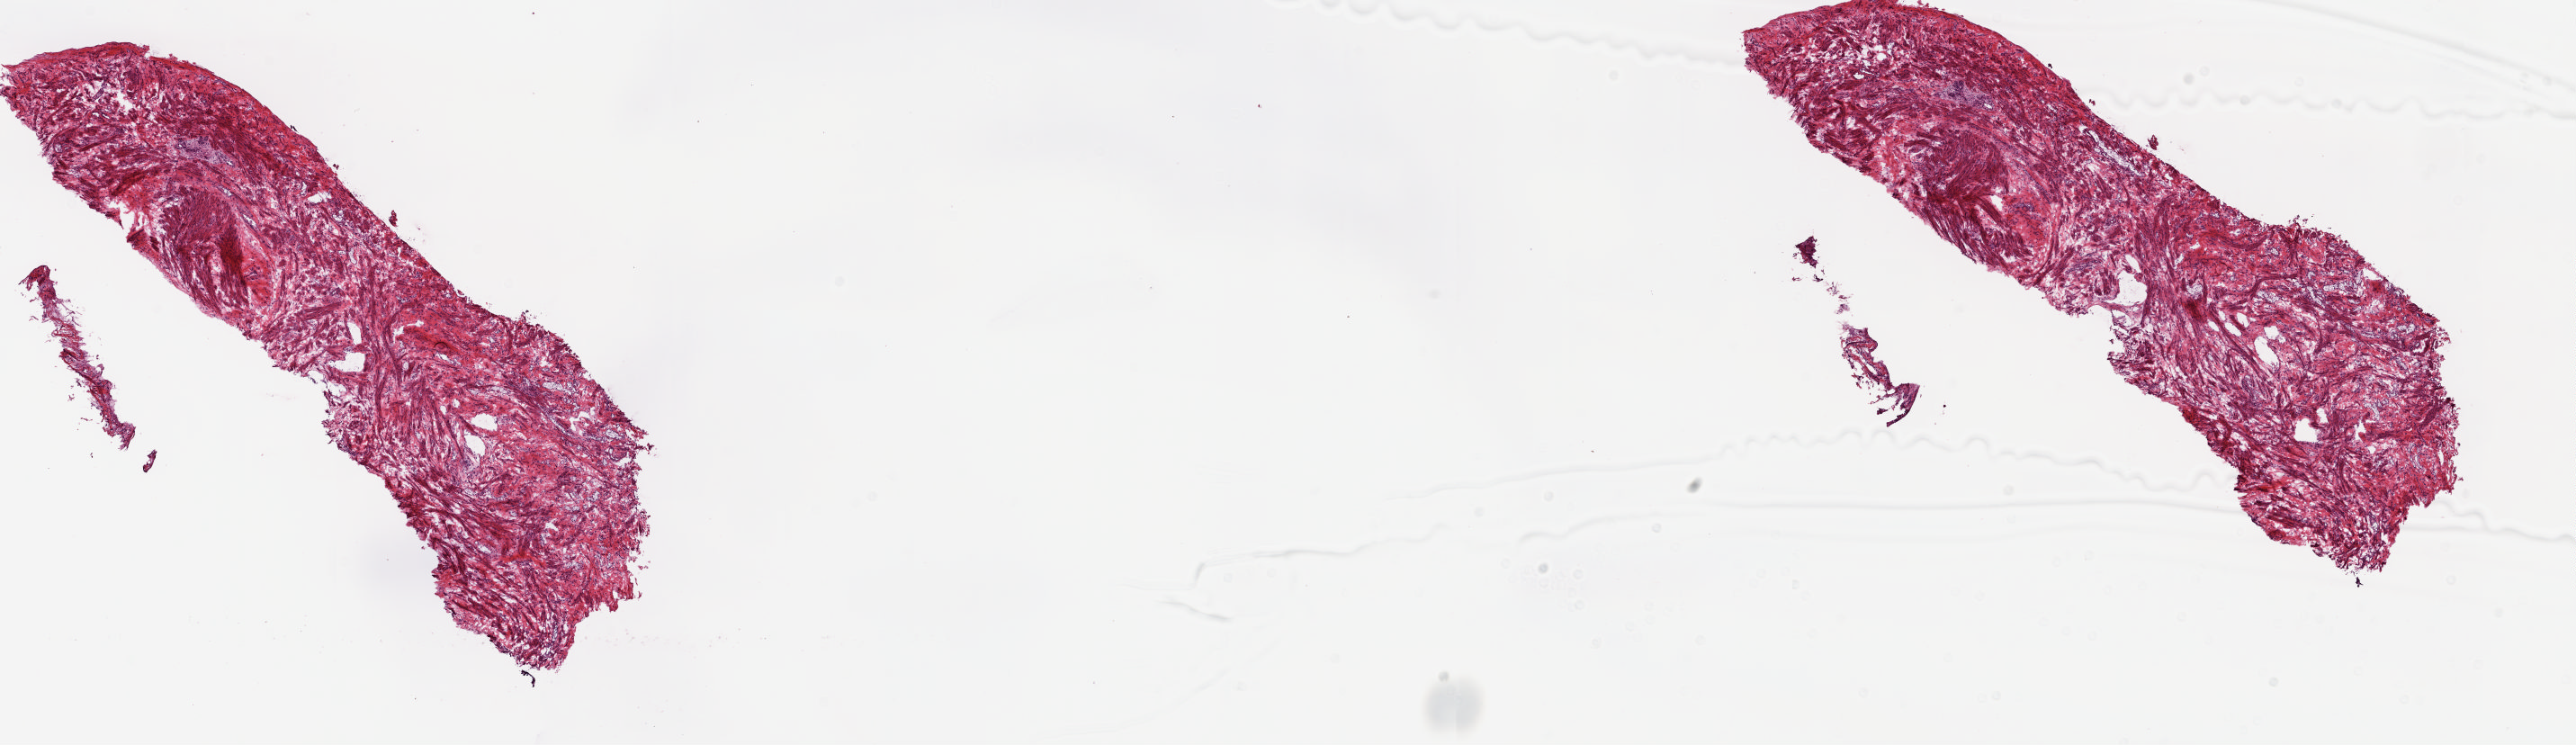
Whole-slide histology image, Hematoxylin and eosin (H&E) stained — low-resolution overview of the scanned area, about 22.7 x 6.6 mm, frozen section from the top of the tissue portion, uterus, solid tissue normal (non-tumour tissue) sample. Female patient; age at initial diagnosis 63 years. Pathologist review of this section (percent, as recorded): tumour cells 0%, tumour nuclei 0%.
This section: solid tissue normal sample (biorepository sample class). Patient diagnosis: Endometrioid adenocarcinoma, NOS (endometrium).